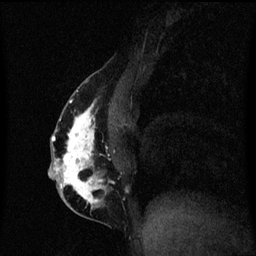
Breast MRI (dynamic contrast-enhanced), one sagittal slice; slice 27 of 60 in the series (ordered by position); dynamic contrast-enhanced series, image 2 of 3 at this slice position (ordered by acquisition); 1.5 T; TE 4.2 ms, TR 8.4 ms; 2 mm slice thickness; 256 × 256 image matrix, field of view 200 × 200 mm. Female patient, age 40 years.
Outlined on this slice (semi-automatically segmented with operator editing):
- analysis volume of interest (the breast-tissue region the enhancement analysis was run in; not a lesion): bounding box [x1, y1, x2, y2] px = [49, 84, 119, 211]
- tumour enhancement mask (voxels above the 70 % enhancement threshold inside the analysis volume of interest): [49, 90, 104, 209]